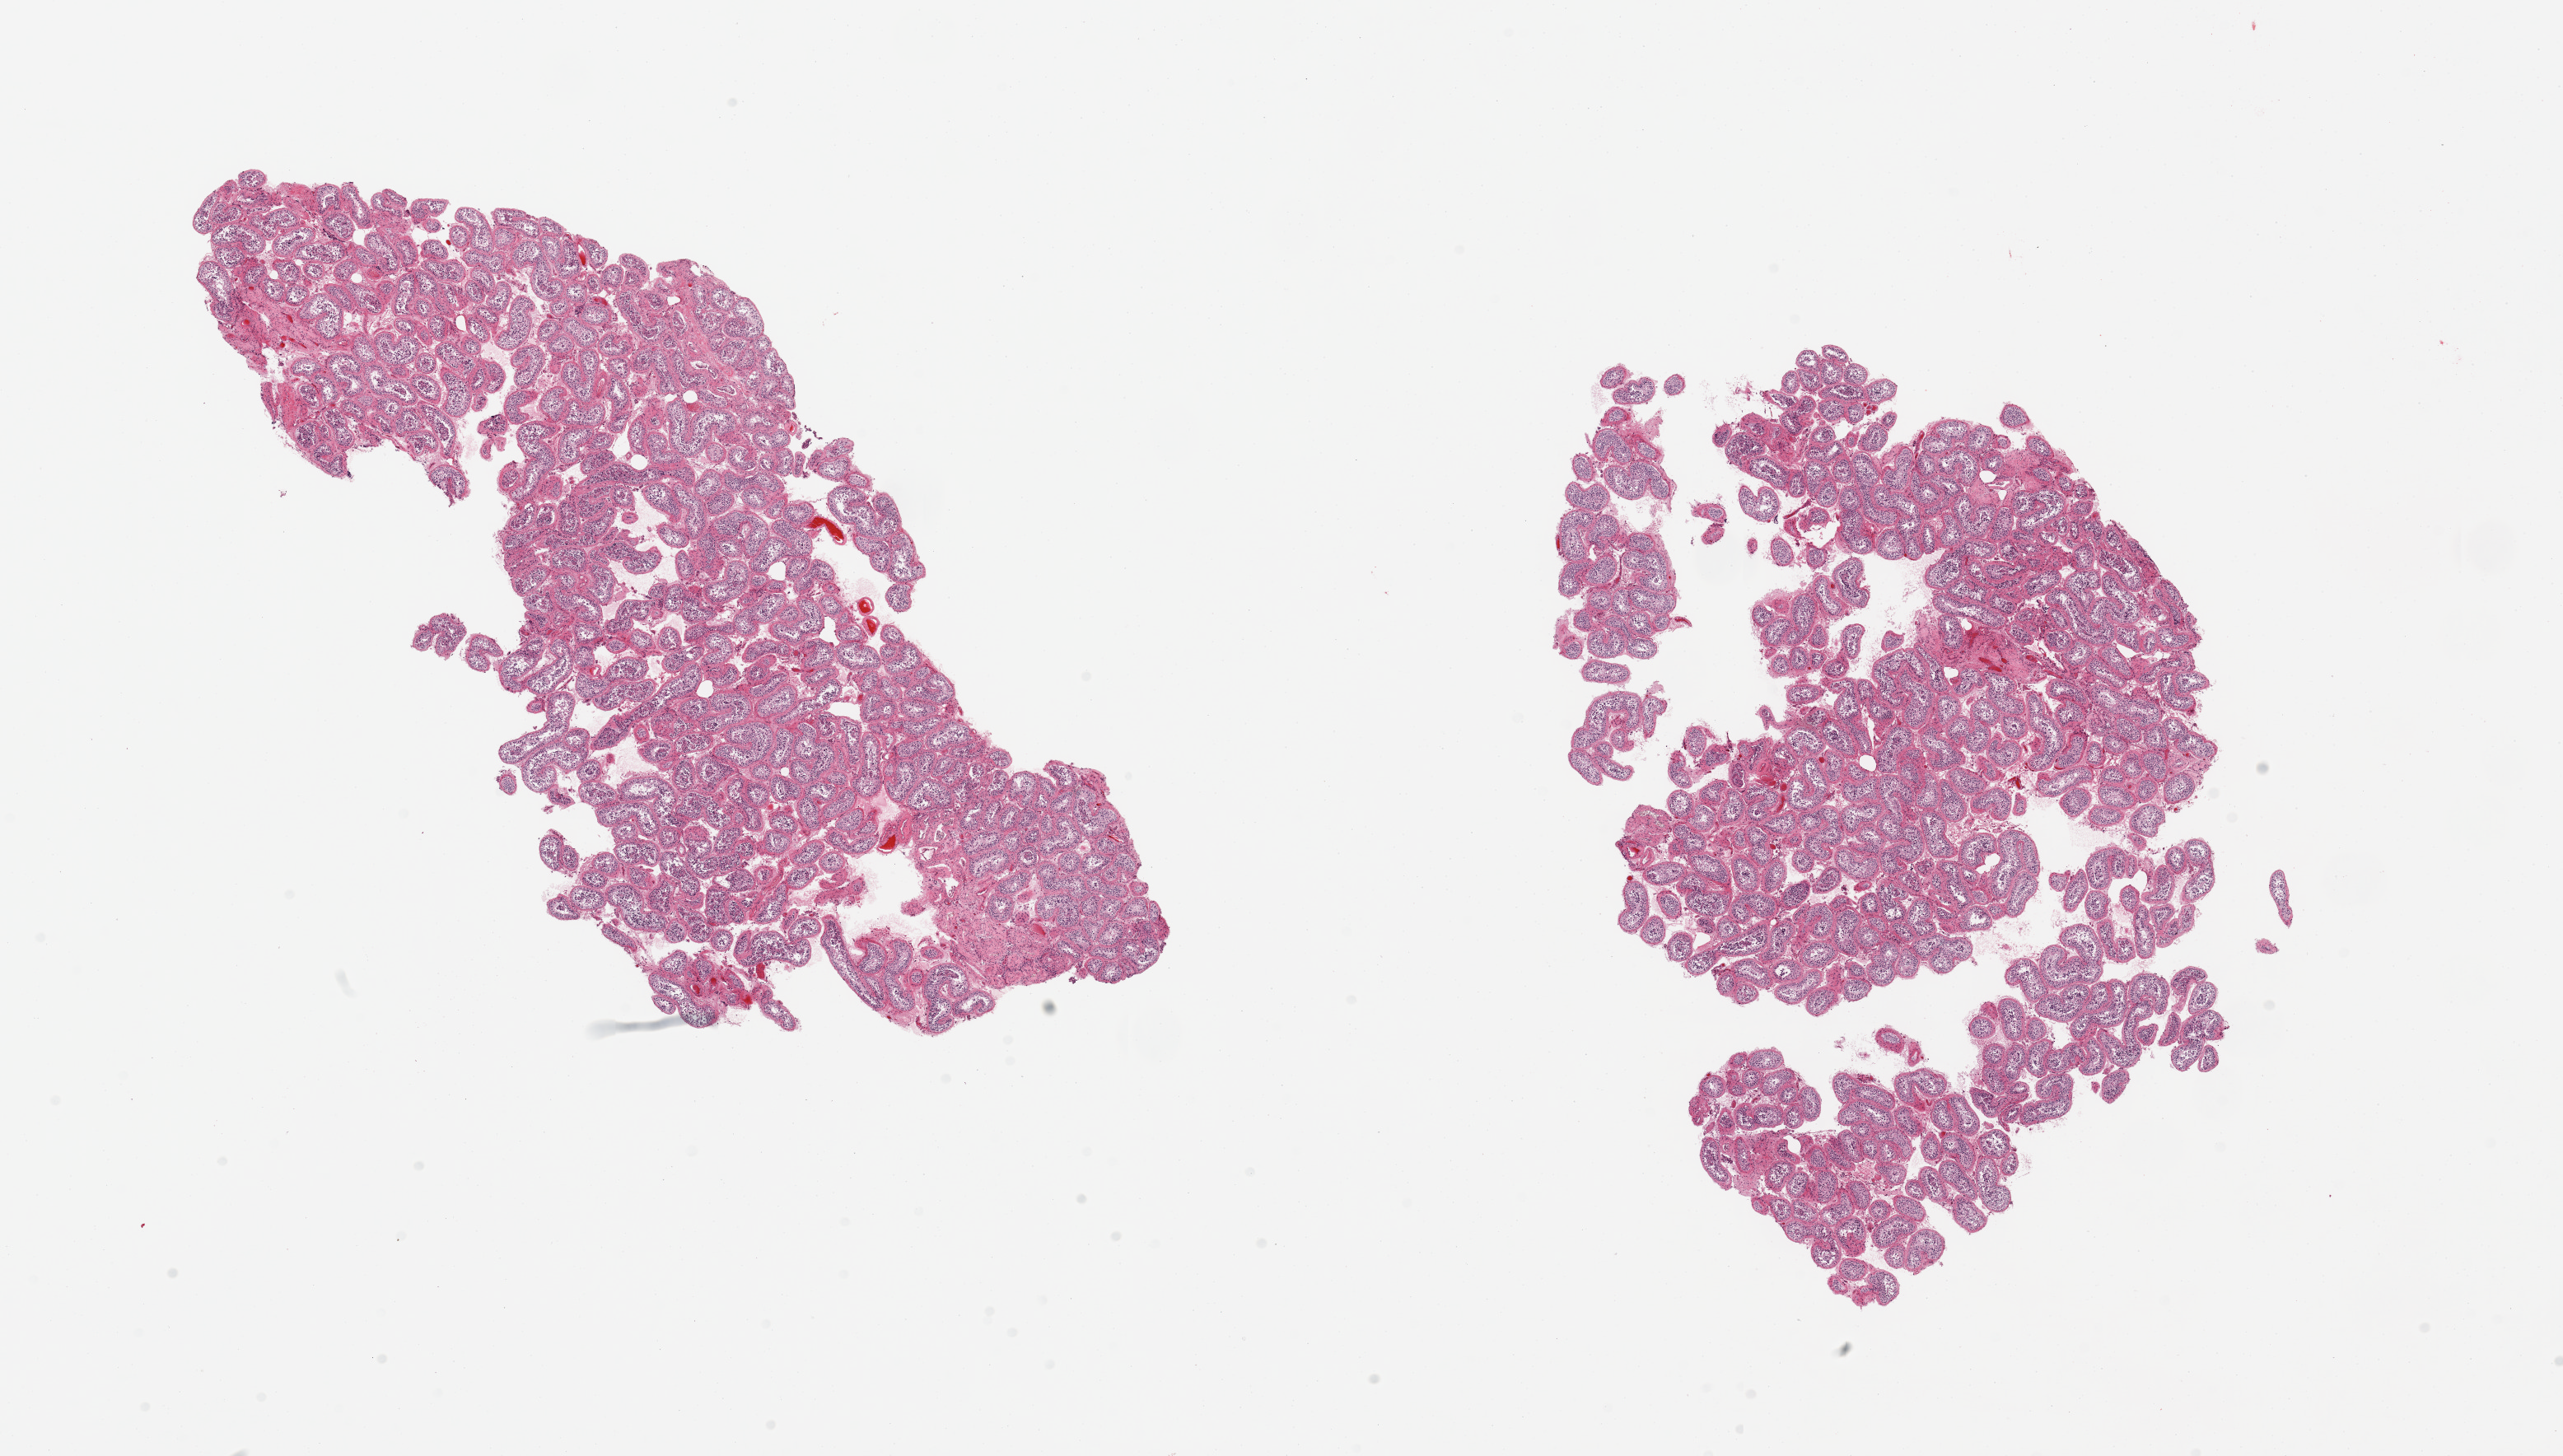
Haematoxylin and eosin whole-slide image — a low-resolution overview of the entire scanned area, about 24.6 x 14.0 mm (slide scanned at 20x). PAXgene-fixed paraffin-embedded (PFPE) section. Section of testis (target tissue). Donor tissue sample. Male donor.
Review note (as recorded): 2 pieces; spermatogenesis is reduced.